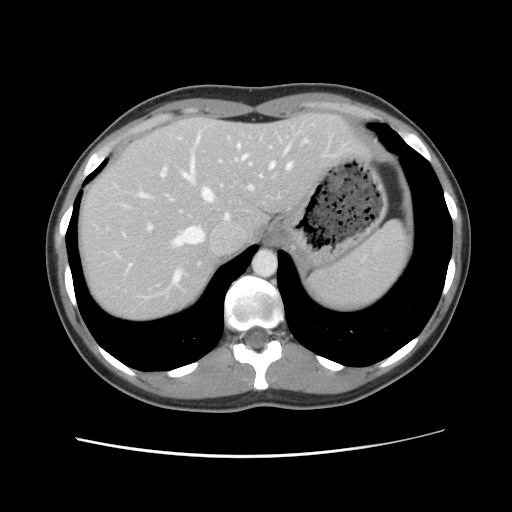
Contrast-enhanced abdominal CT, one axial slice; slice 93 of 134 in the series (ordered by position); 120 kVp; intravenous contrast given; soft-tissue window (W 400 / L 40 HU); 2.5 mm slice thickness; 512 × 512 image matrix, field of view 339 × 339 mm. Female patient, age 33 years. From the clinical record (not read from this slice): diagnosis: colorectal cancer liver metastases, imaged before liver resection; multiple liver metastases: yes; largest metastasis: 4.5 cm; disease in both lobes: yes.
Structures marked on this image (manually delineated by an expert):
- hepatic veins: bounding box <130,133,307,283> (left, top, right, bottom; pixels)
- liver: <78,114,366,322>
- planned liver remnant (the part of the liver to remain after resection): <78,114,365,322>
- portal vein (with intrahepatic branches): <119,146,272,232>